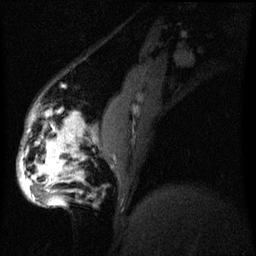
Breast MRI (dynamic contrast-enhanced), one sagittal slice; slice 17 of 60 in the series (ordered by position); dynamic contrast-enhanced series, image 2 of 3 at this slice position (ordered by acquisition); 1.5 T; TE 4.2 ms, TR 8 ms; 2.2 mm slice thickness; 256 × 256 image matrix, field of view 200 × 200 mm. Patient: female, 50 years.
Structures marked on this image (semi-automatic segmentation, software-assisted and operator-edited):
- analysis volume of interest (the breast-tissue region the enhancement analysis was run in; not a lesion): box from (x=19, y=112) to (x=76, y=209) px
- tumour enhancement mask (voxels above the 70 % enhancement threshold inside the analysis volume of interest): (x=21, y=120)–(x=74, y=205)